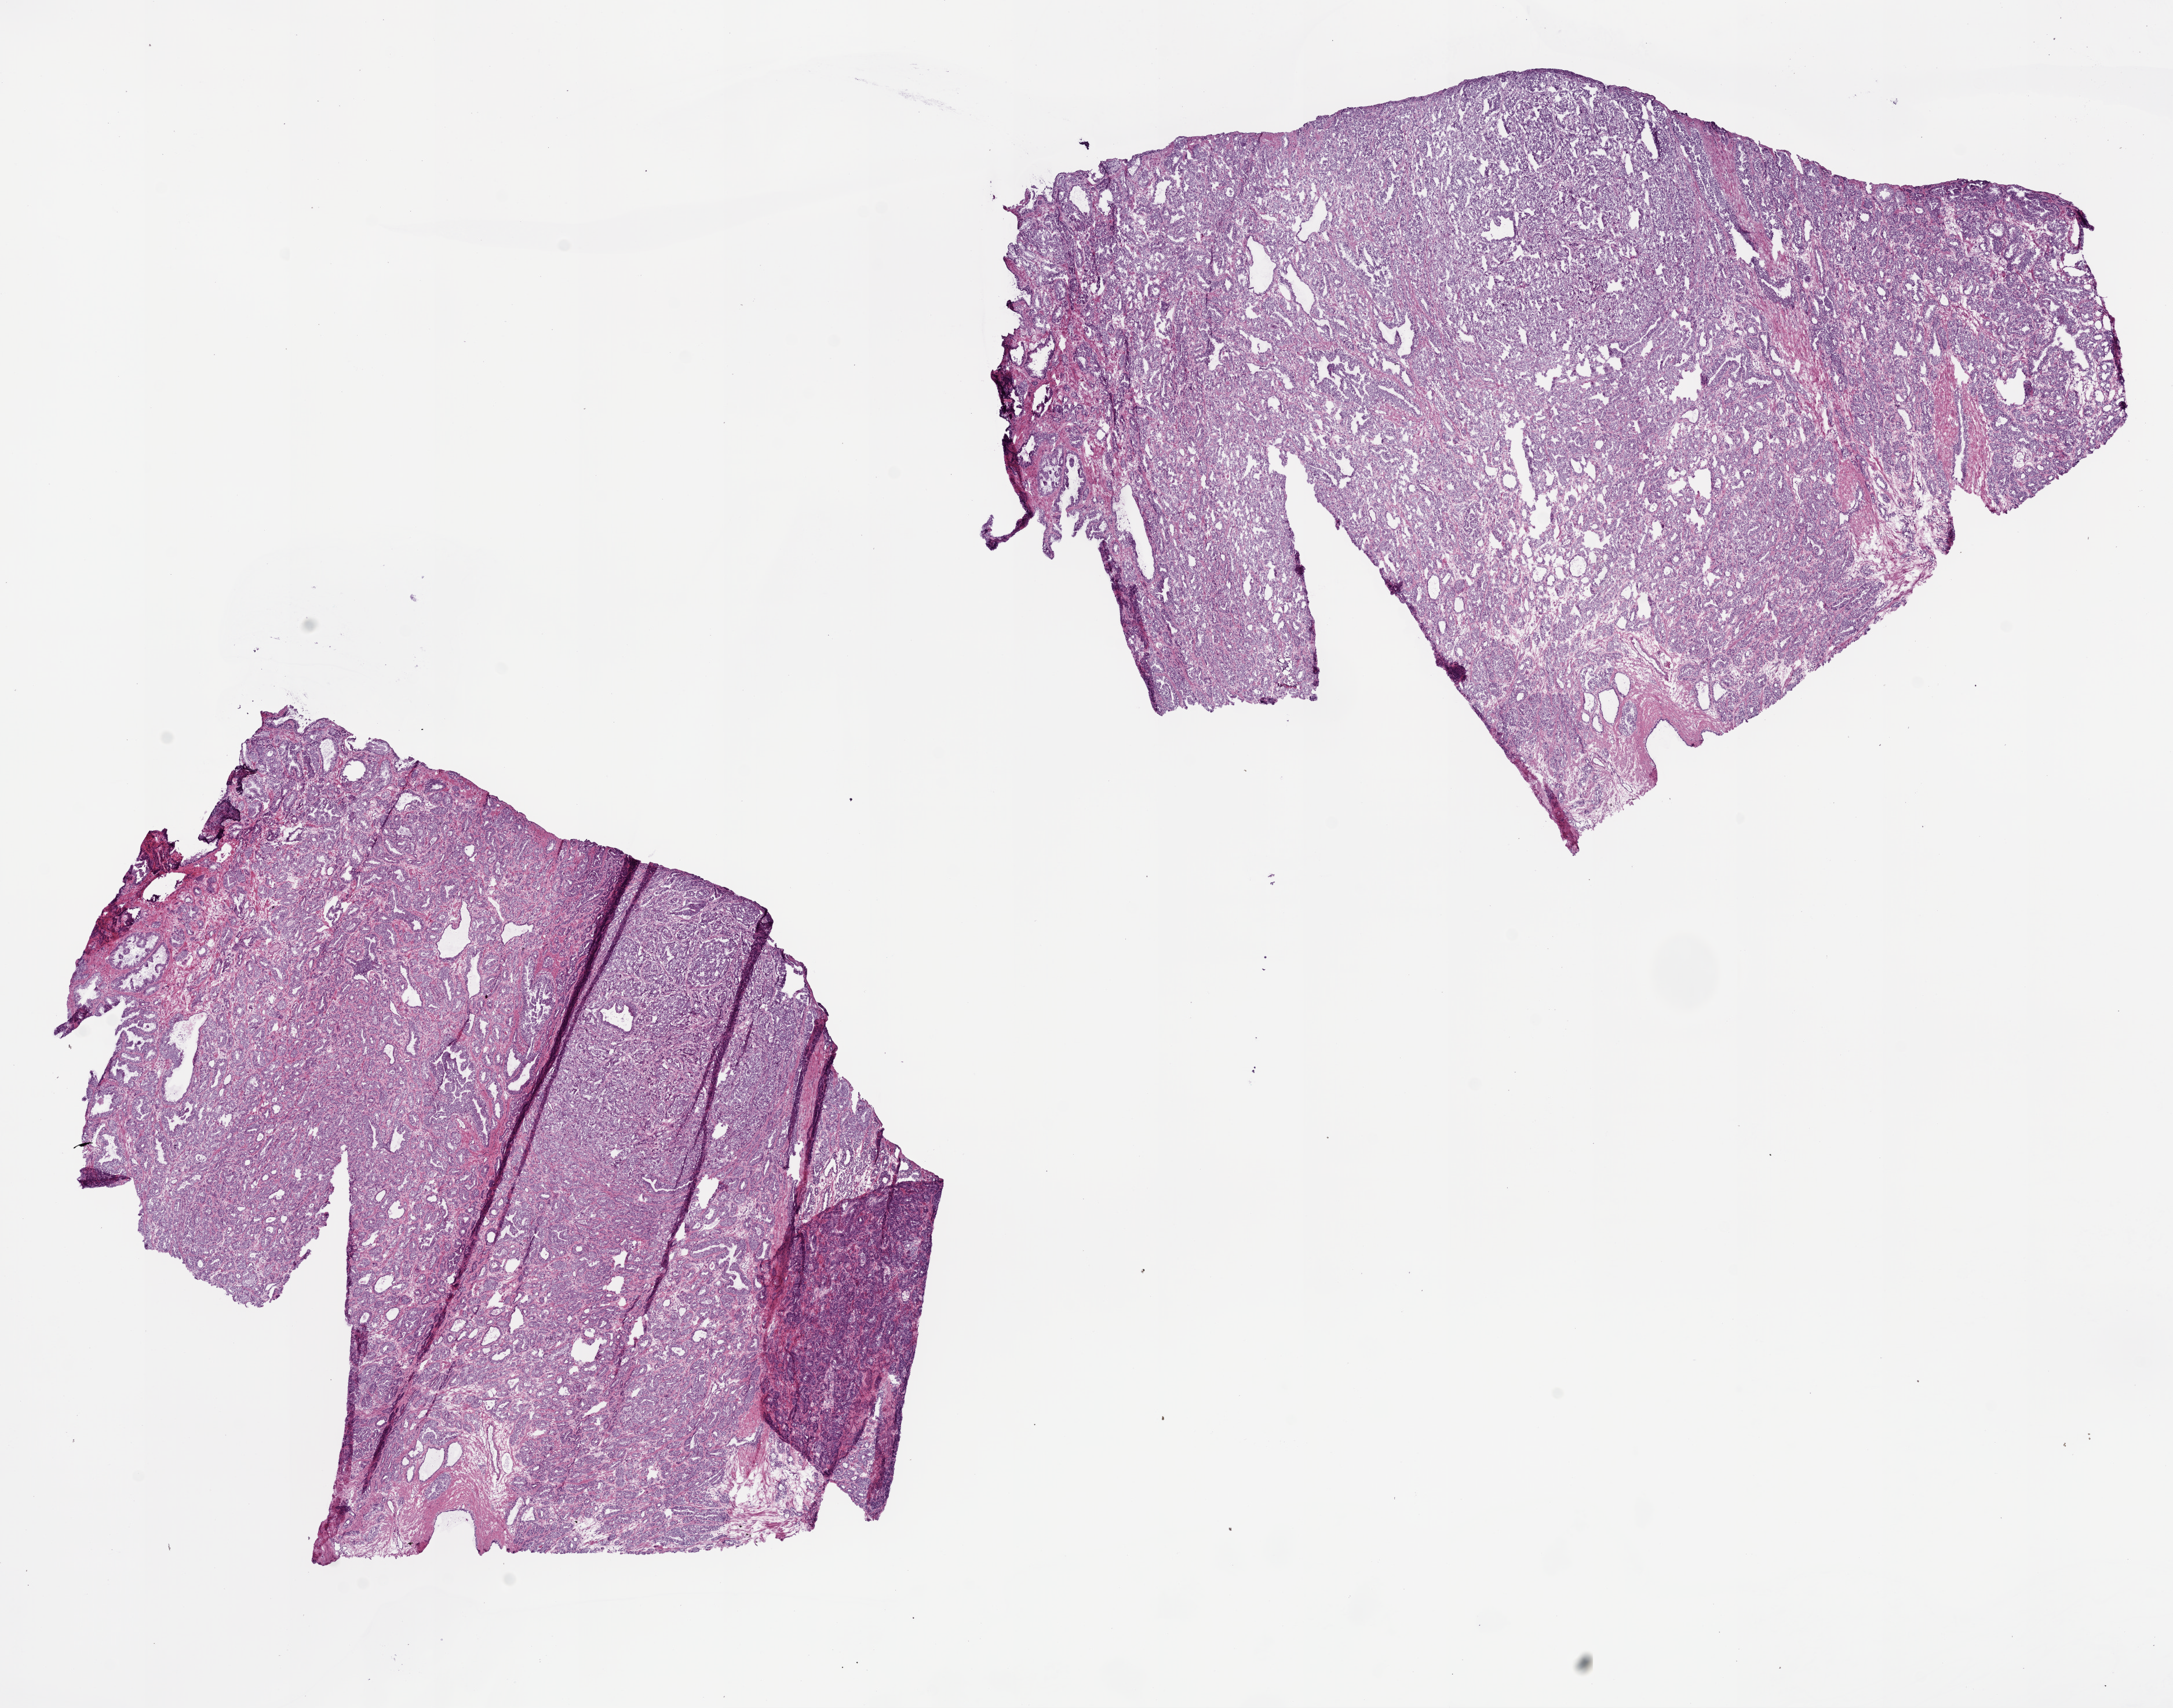
Digitized H&E-stained tissue section (whole slide) — shown as a low-resolution overview of the whole scanned area (about 15.0 x 11.8 mm, acquisition: 20x scan). Frozen section from the bottom of the tissue portion. Sample: primary tumour, prostate. Male, age 57 years at initial diagnosis. Gleason score: 7 (4+3). Slide review estimates, as recorded: tumour cells 70%, tumour nuclei 80%, normal cells 15%, stromal cells 15%, necrosis 0%. Inflammatory infiltration, as recorded: lymphocyte infiltration 0%, monocyte infiltration 0%, neutrophil infiltration 0%.
- lymph nodes positive (case pathology): 0 of 24 examined
- diagnosis: Acinar cell carcinoma